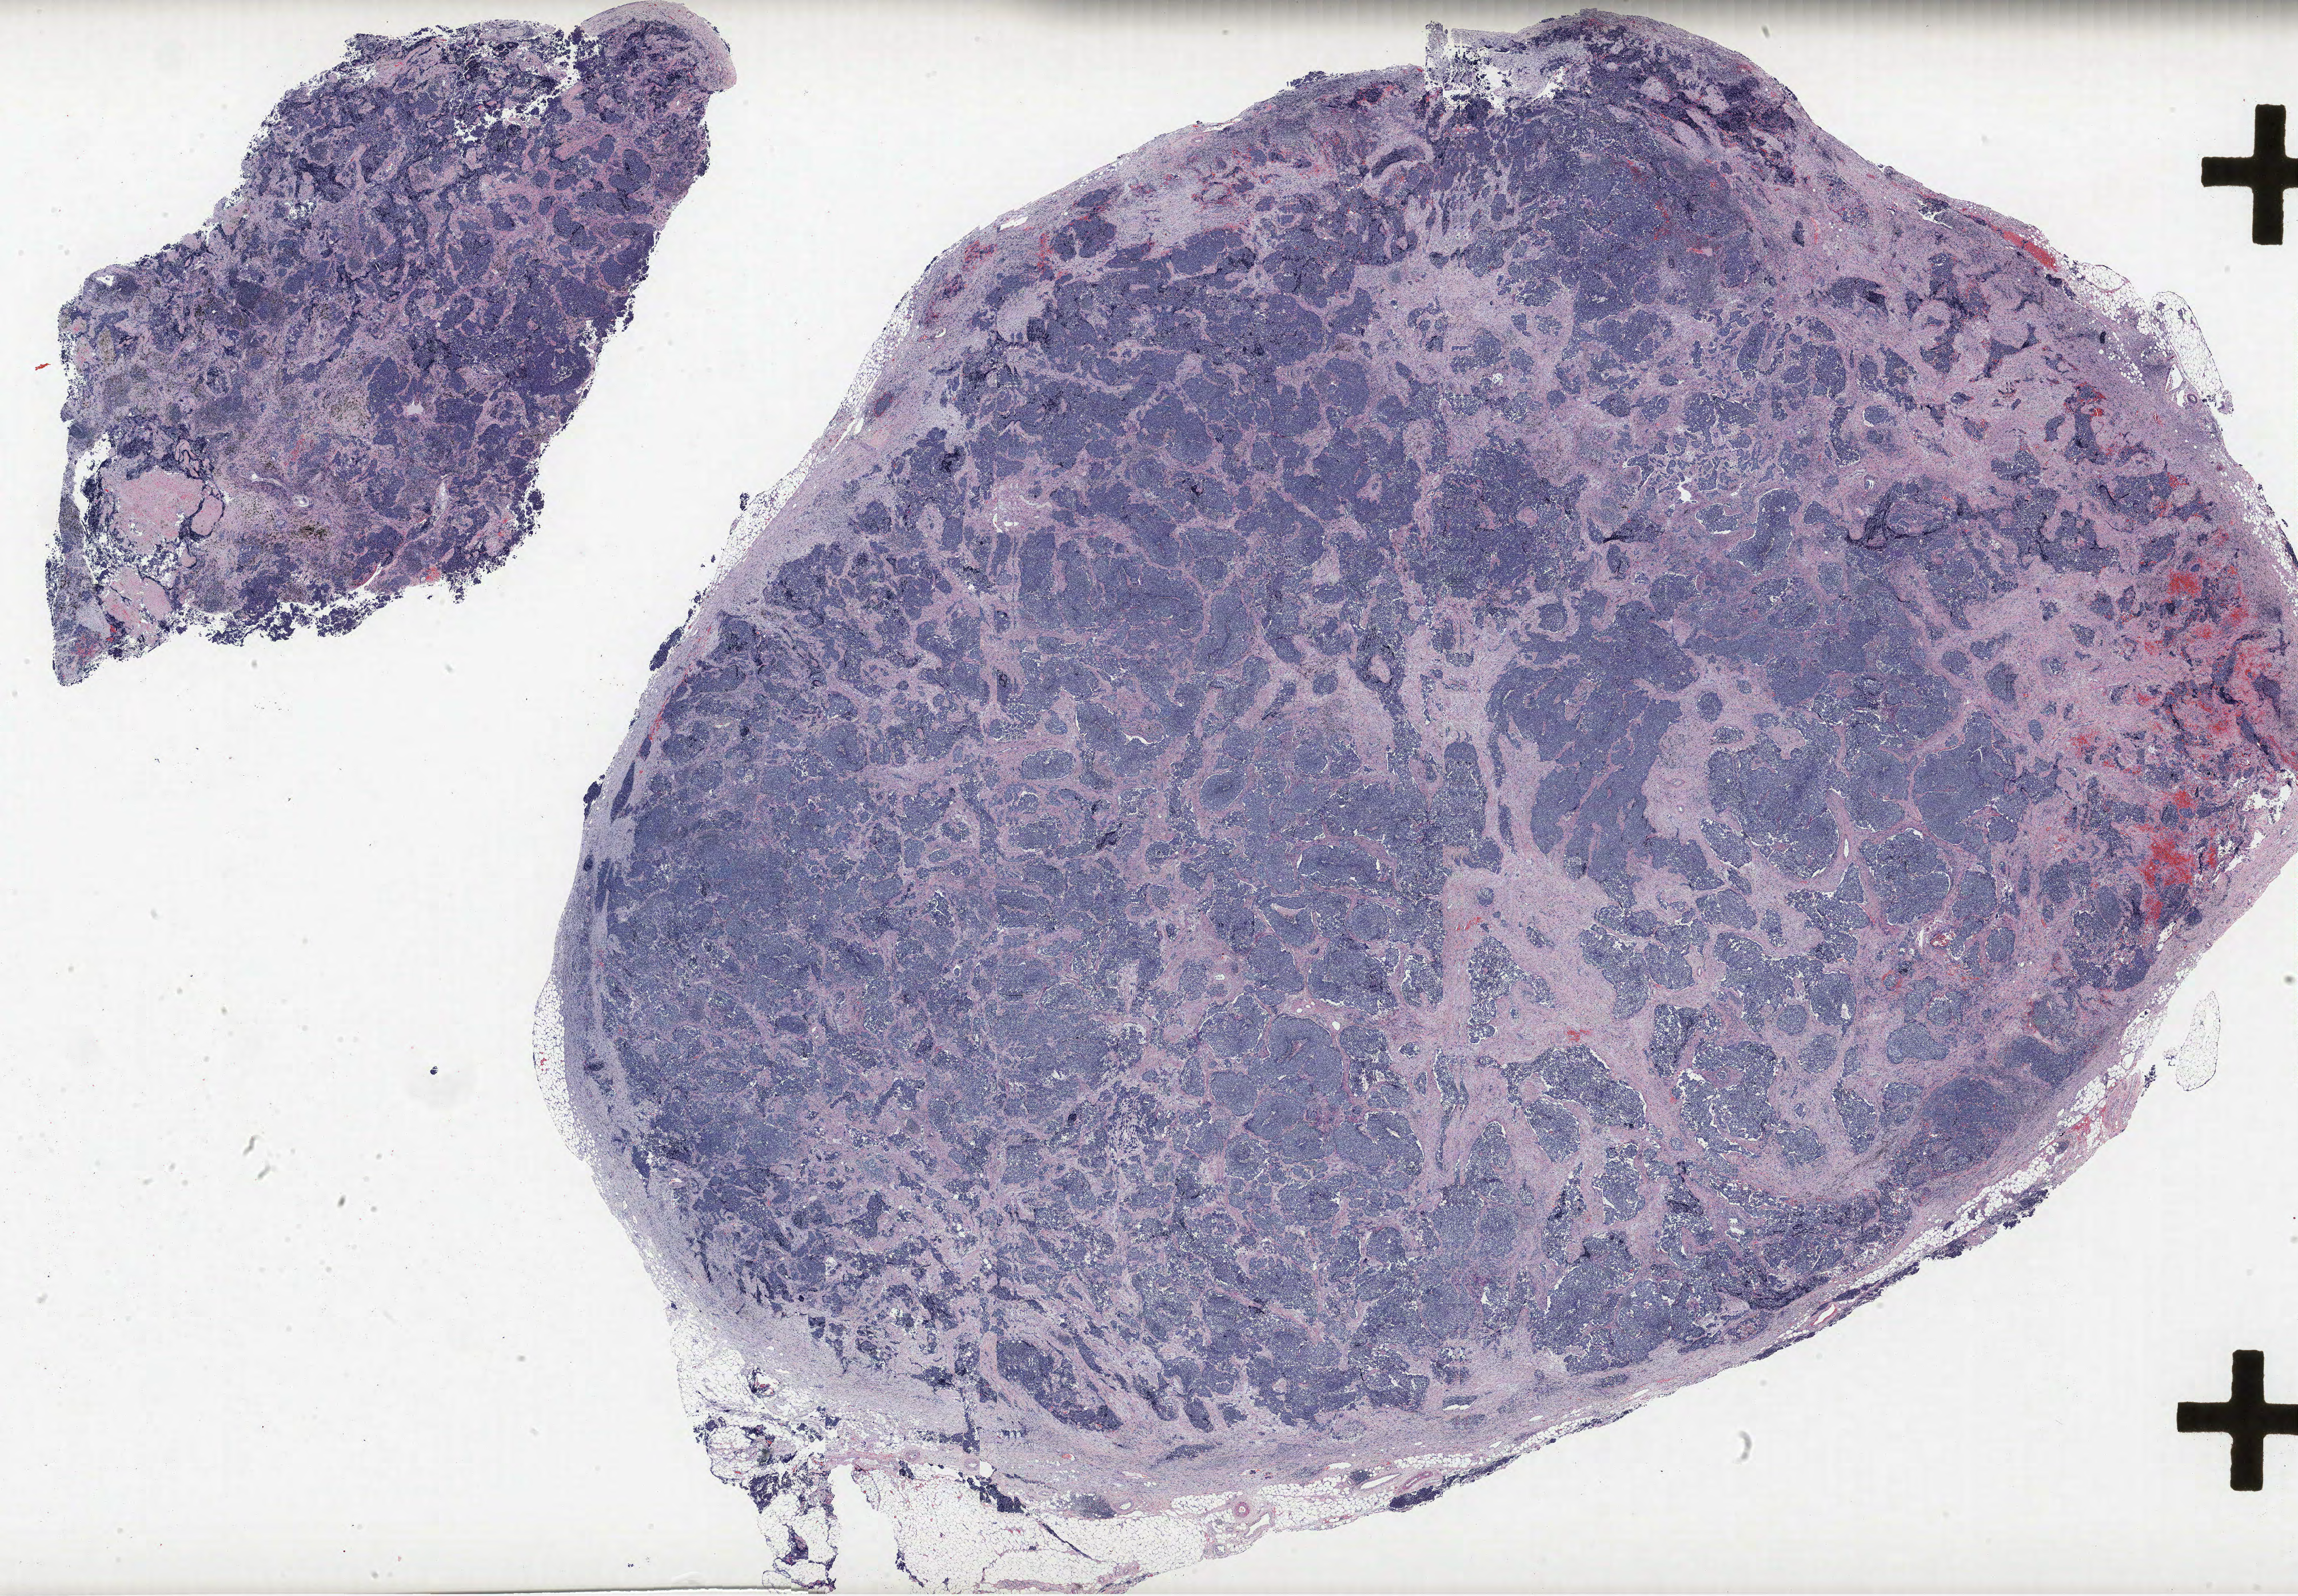
Whole-slide histology image, H&E-stained — a low-resolution overview of the entire scanned area, about 32.2 x 22.3 mm (from a 40x scan); FFPE section; lung. Male, age 73 at enrolment. Current smoker at enrolment. Grade: cannot be assessed (GX).
Tumour size (pathology): 19 mm. Participant's lung-cancer diagnosis: Small cell carcinoma, NOS. Primary tumour location (clinical record): left upper lobe. Stage (AJCC 6th edition): IIIB.